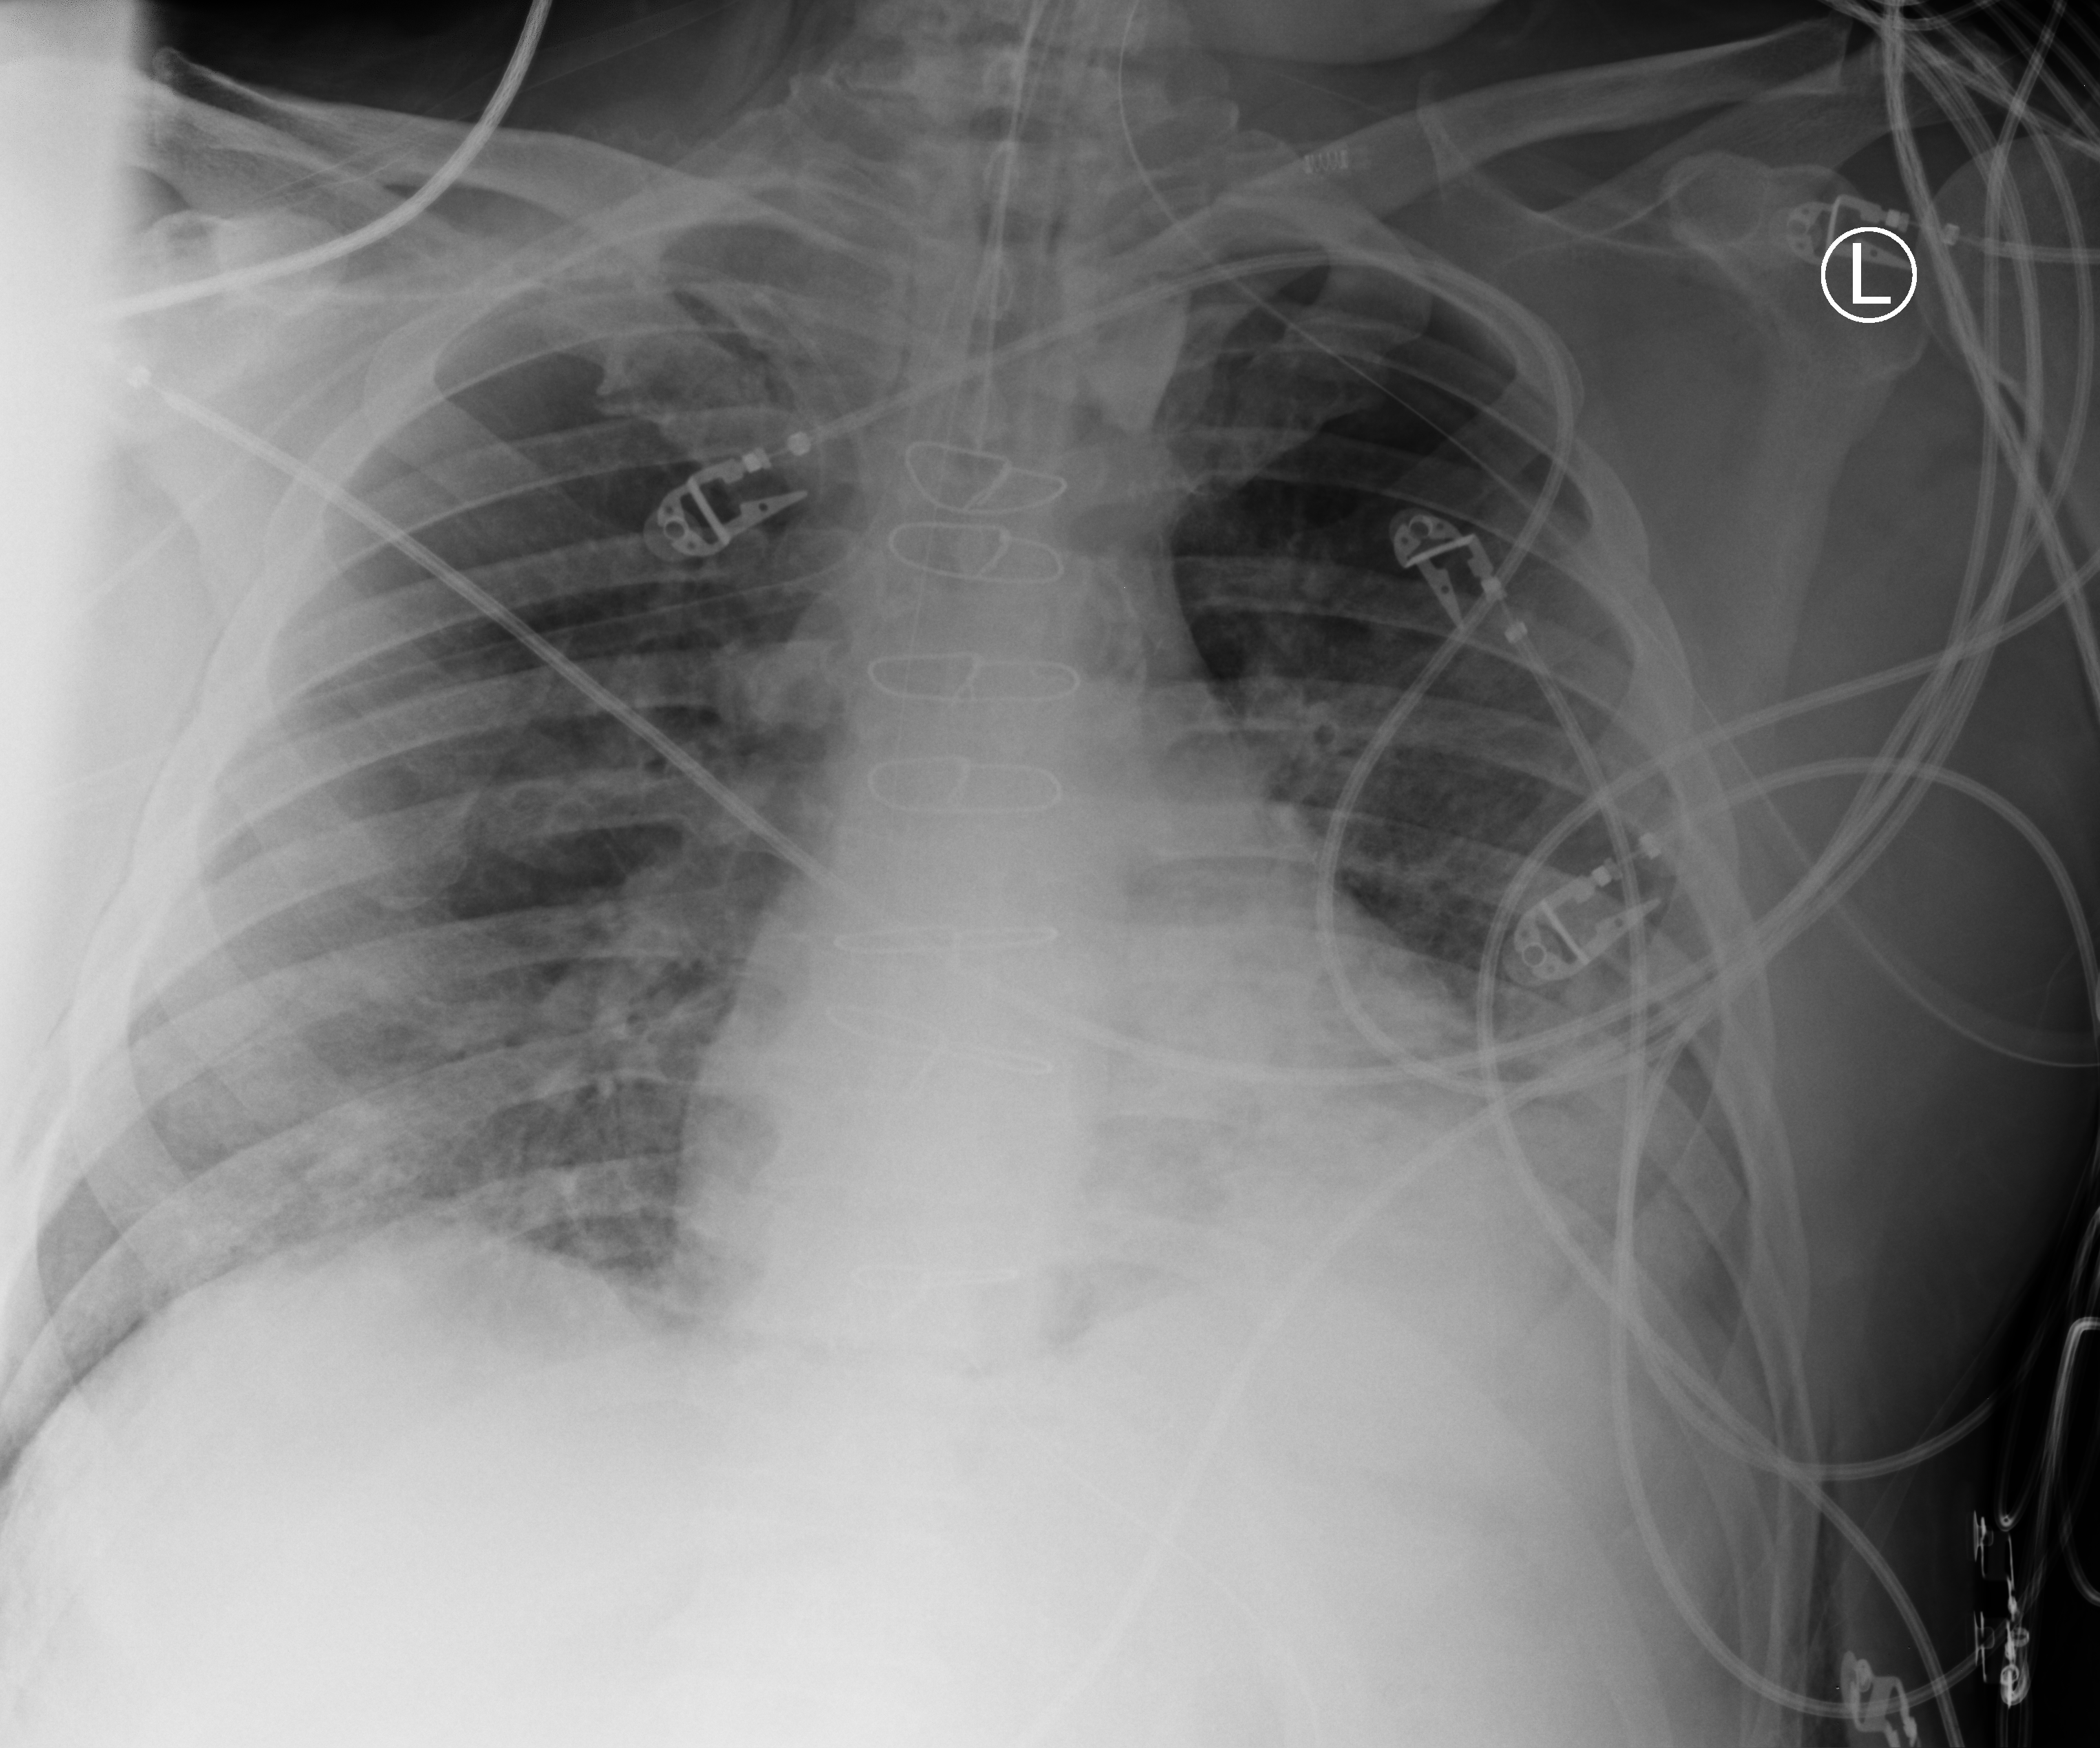
Chest X-ray (portable), anteroposterior (AP) projection. Male patient hospitalised with COVID-19, age 60–74 years.
Admission-level facts for this patient (not findings on this image; timing relative to this image not recorded): other chronic lung disease (admission record): no; admitted to intensive care during this hospital stay: yes.